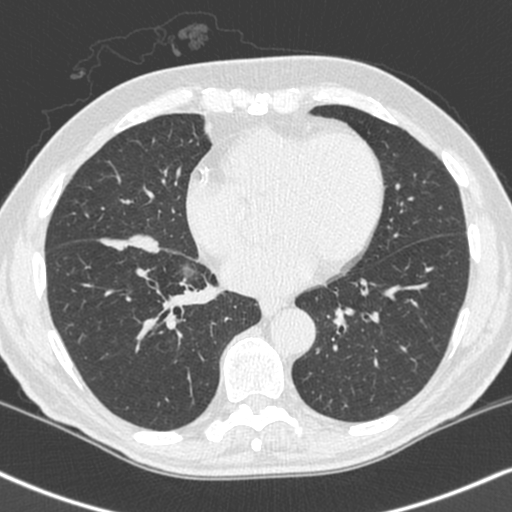
Chest CT (low-dose screening protocol), one axial image, first (baseline) screen, lung window (W 1500 / L -600 HU), 1.3 mm slice thickness, standard (soft-tissue) reconstruction kernel (C), 120 kVp, 512 × 512 image matrix. Male participant, aged 68 years at enrolment.
- Lesion marked by an expert reader, box from (x=90, y=229) to (x=165, y=300) px.
- Reader record for this screening exam (exam-level; its link to the box is not recorded): non-calcified nodule or mass ≥4 mm, right lower lobe, 34 × 17 mm, smooth margins, soft tissue attenuation.
- Official screen result: positive, change unspecified: nodule(s) >= 4 mm or enlarging nodule(s), mass(es), or other non-specific abnormalities suspicious for lung cancer.
- Later outcome: lung cancer diagnosed 24 days after this screen — combined small cell carcinoma, right lower lobe, stage IIIA (AJCC 6th edition), 41 mm at pathology.